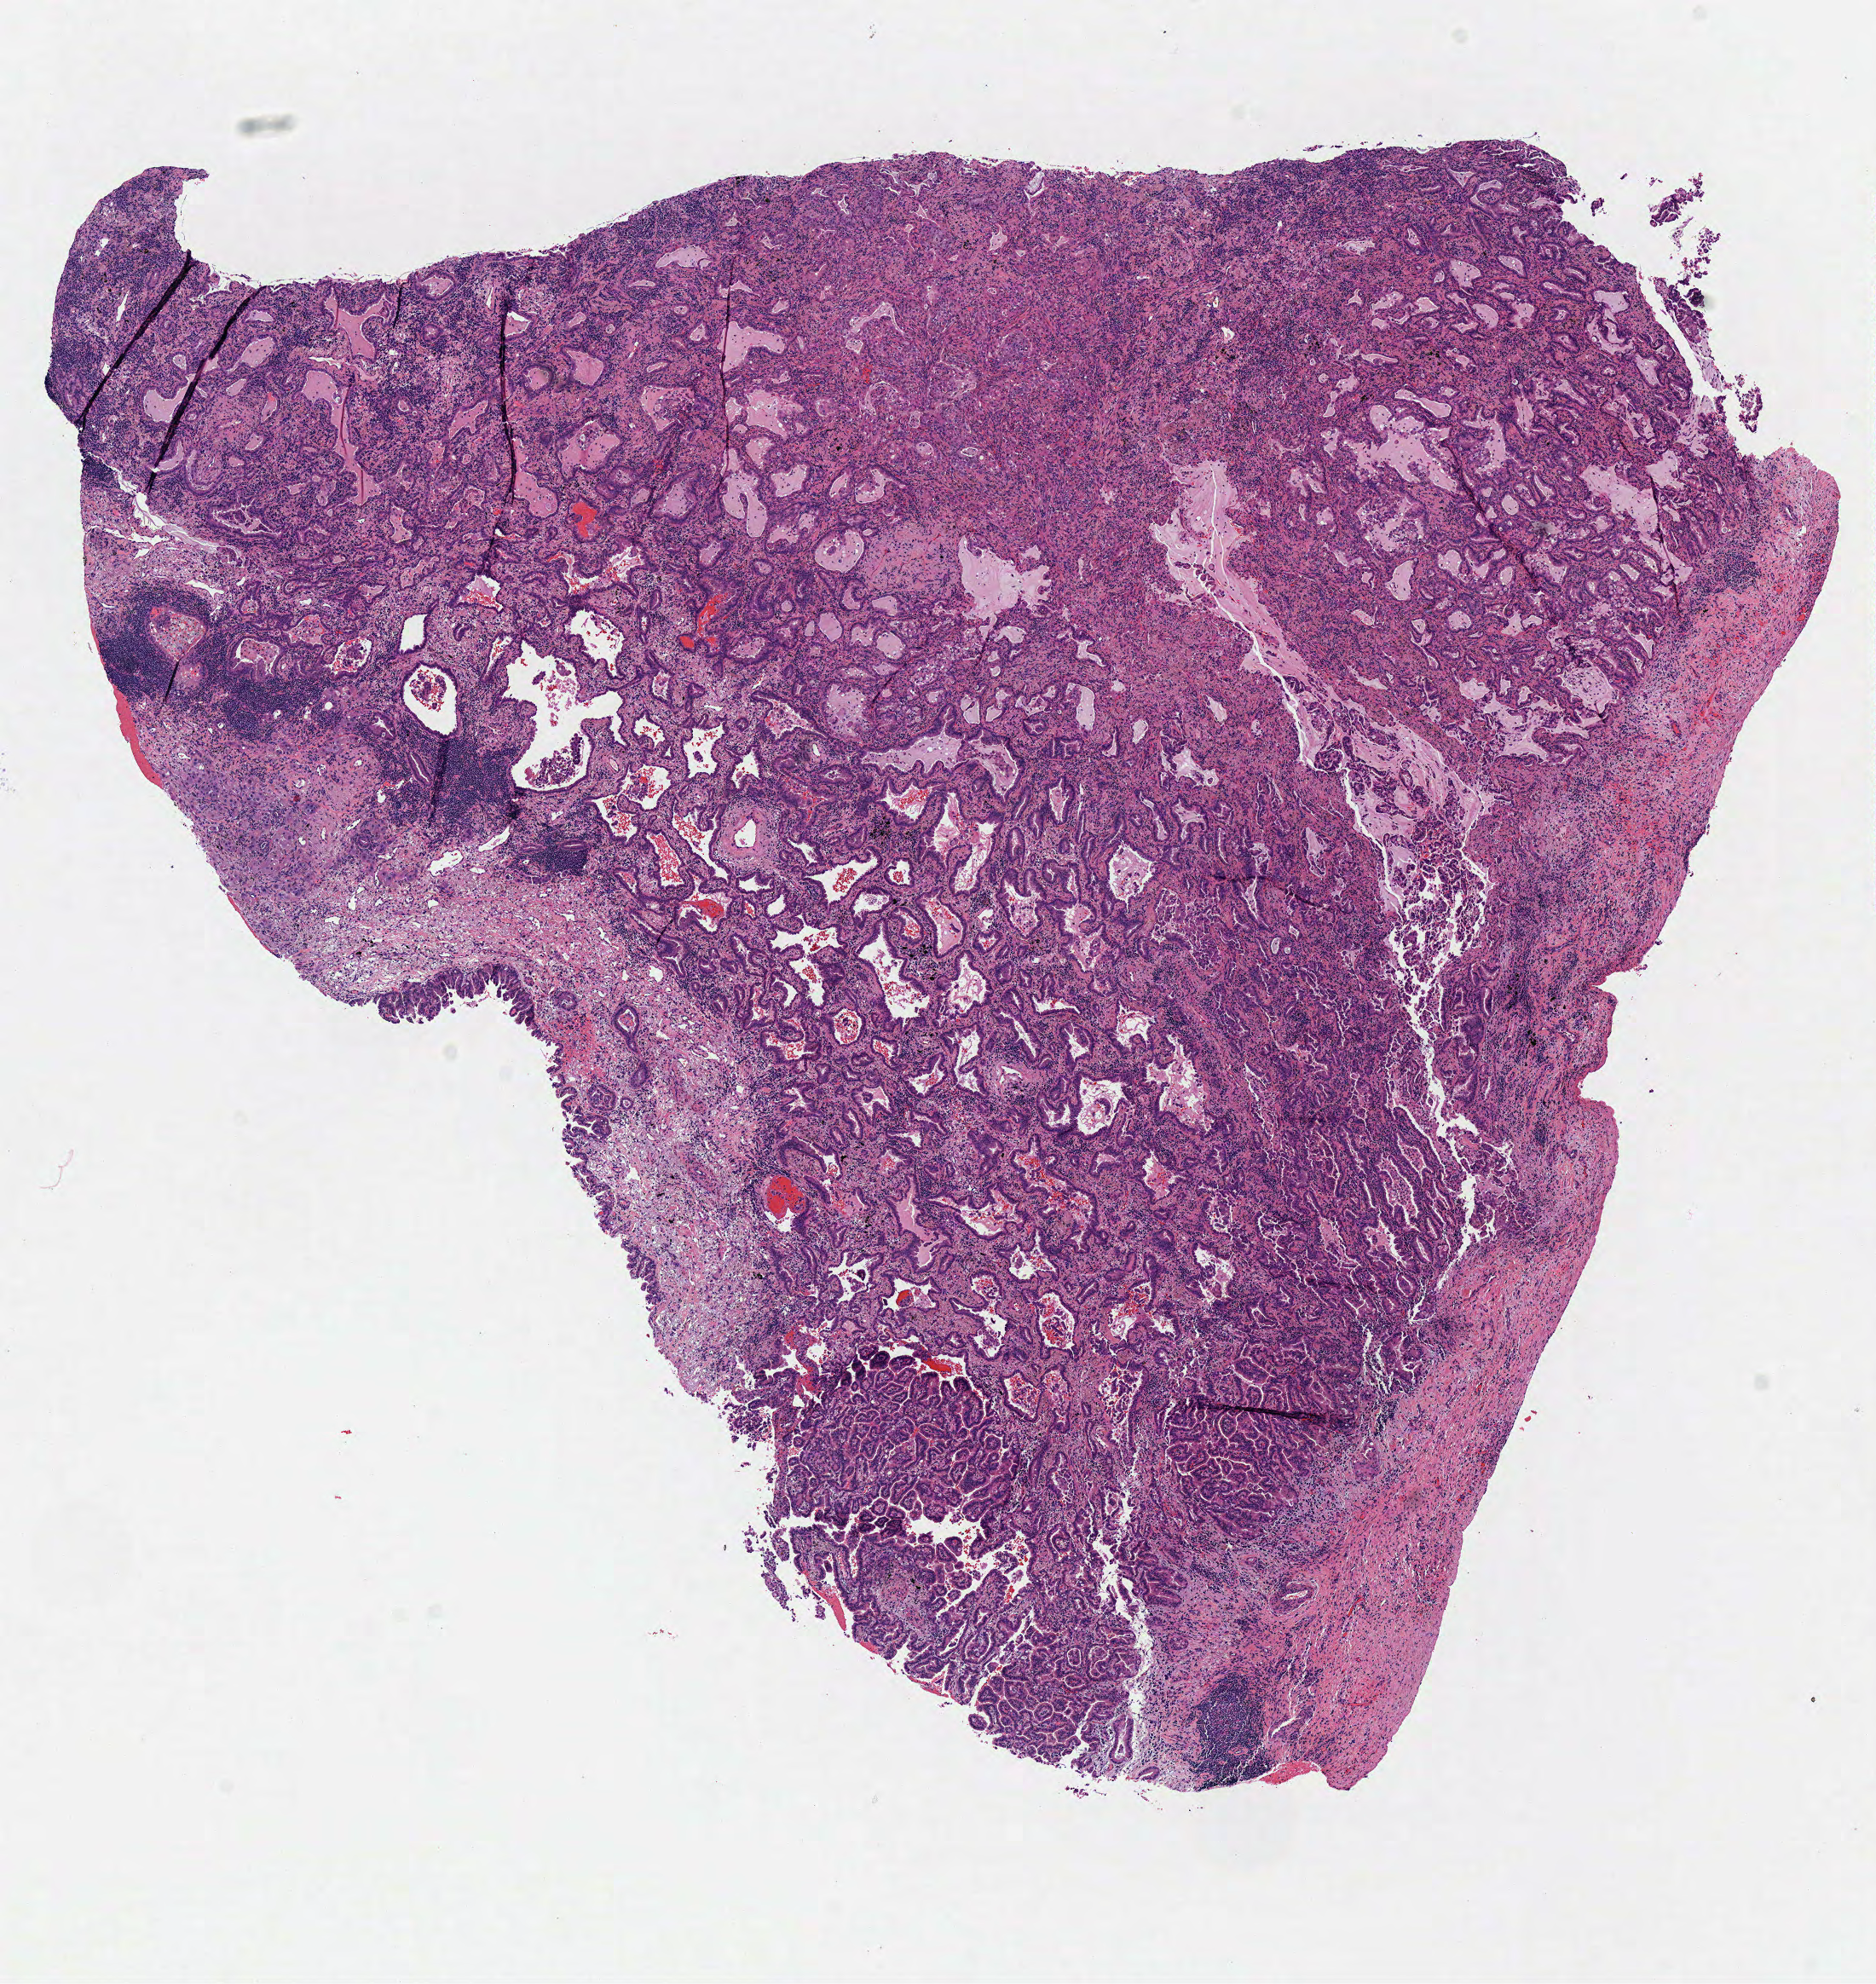
Whole-slide histology image, H&E-stained — a low-resolution overview of the entire scanned area, about 8.7 x 9.2 mm; frozen section from the top of the tissue portion; primary tumour sample from the lung. Patient: female, age at initial diagnosis 75 years. Composition of this section per pathologist review: tumour cells 82%, tumour nuclei 75%, normal cells 0%, stromal cells 15%, necrosis 3%.
Diagnosis: Adenocarcinoma, NOS. Laterality: left. AJCC pathologic stage: IIIA.